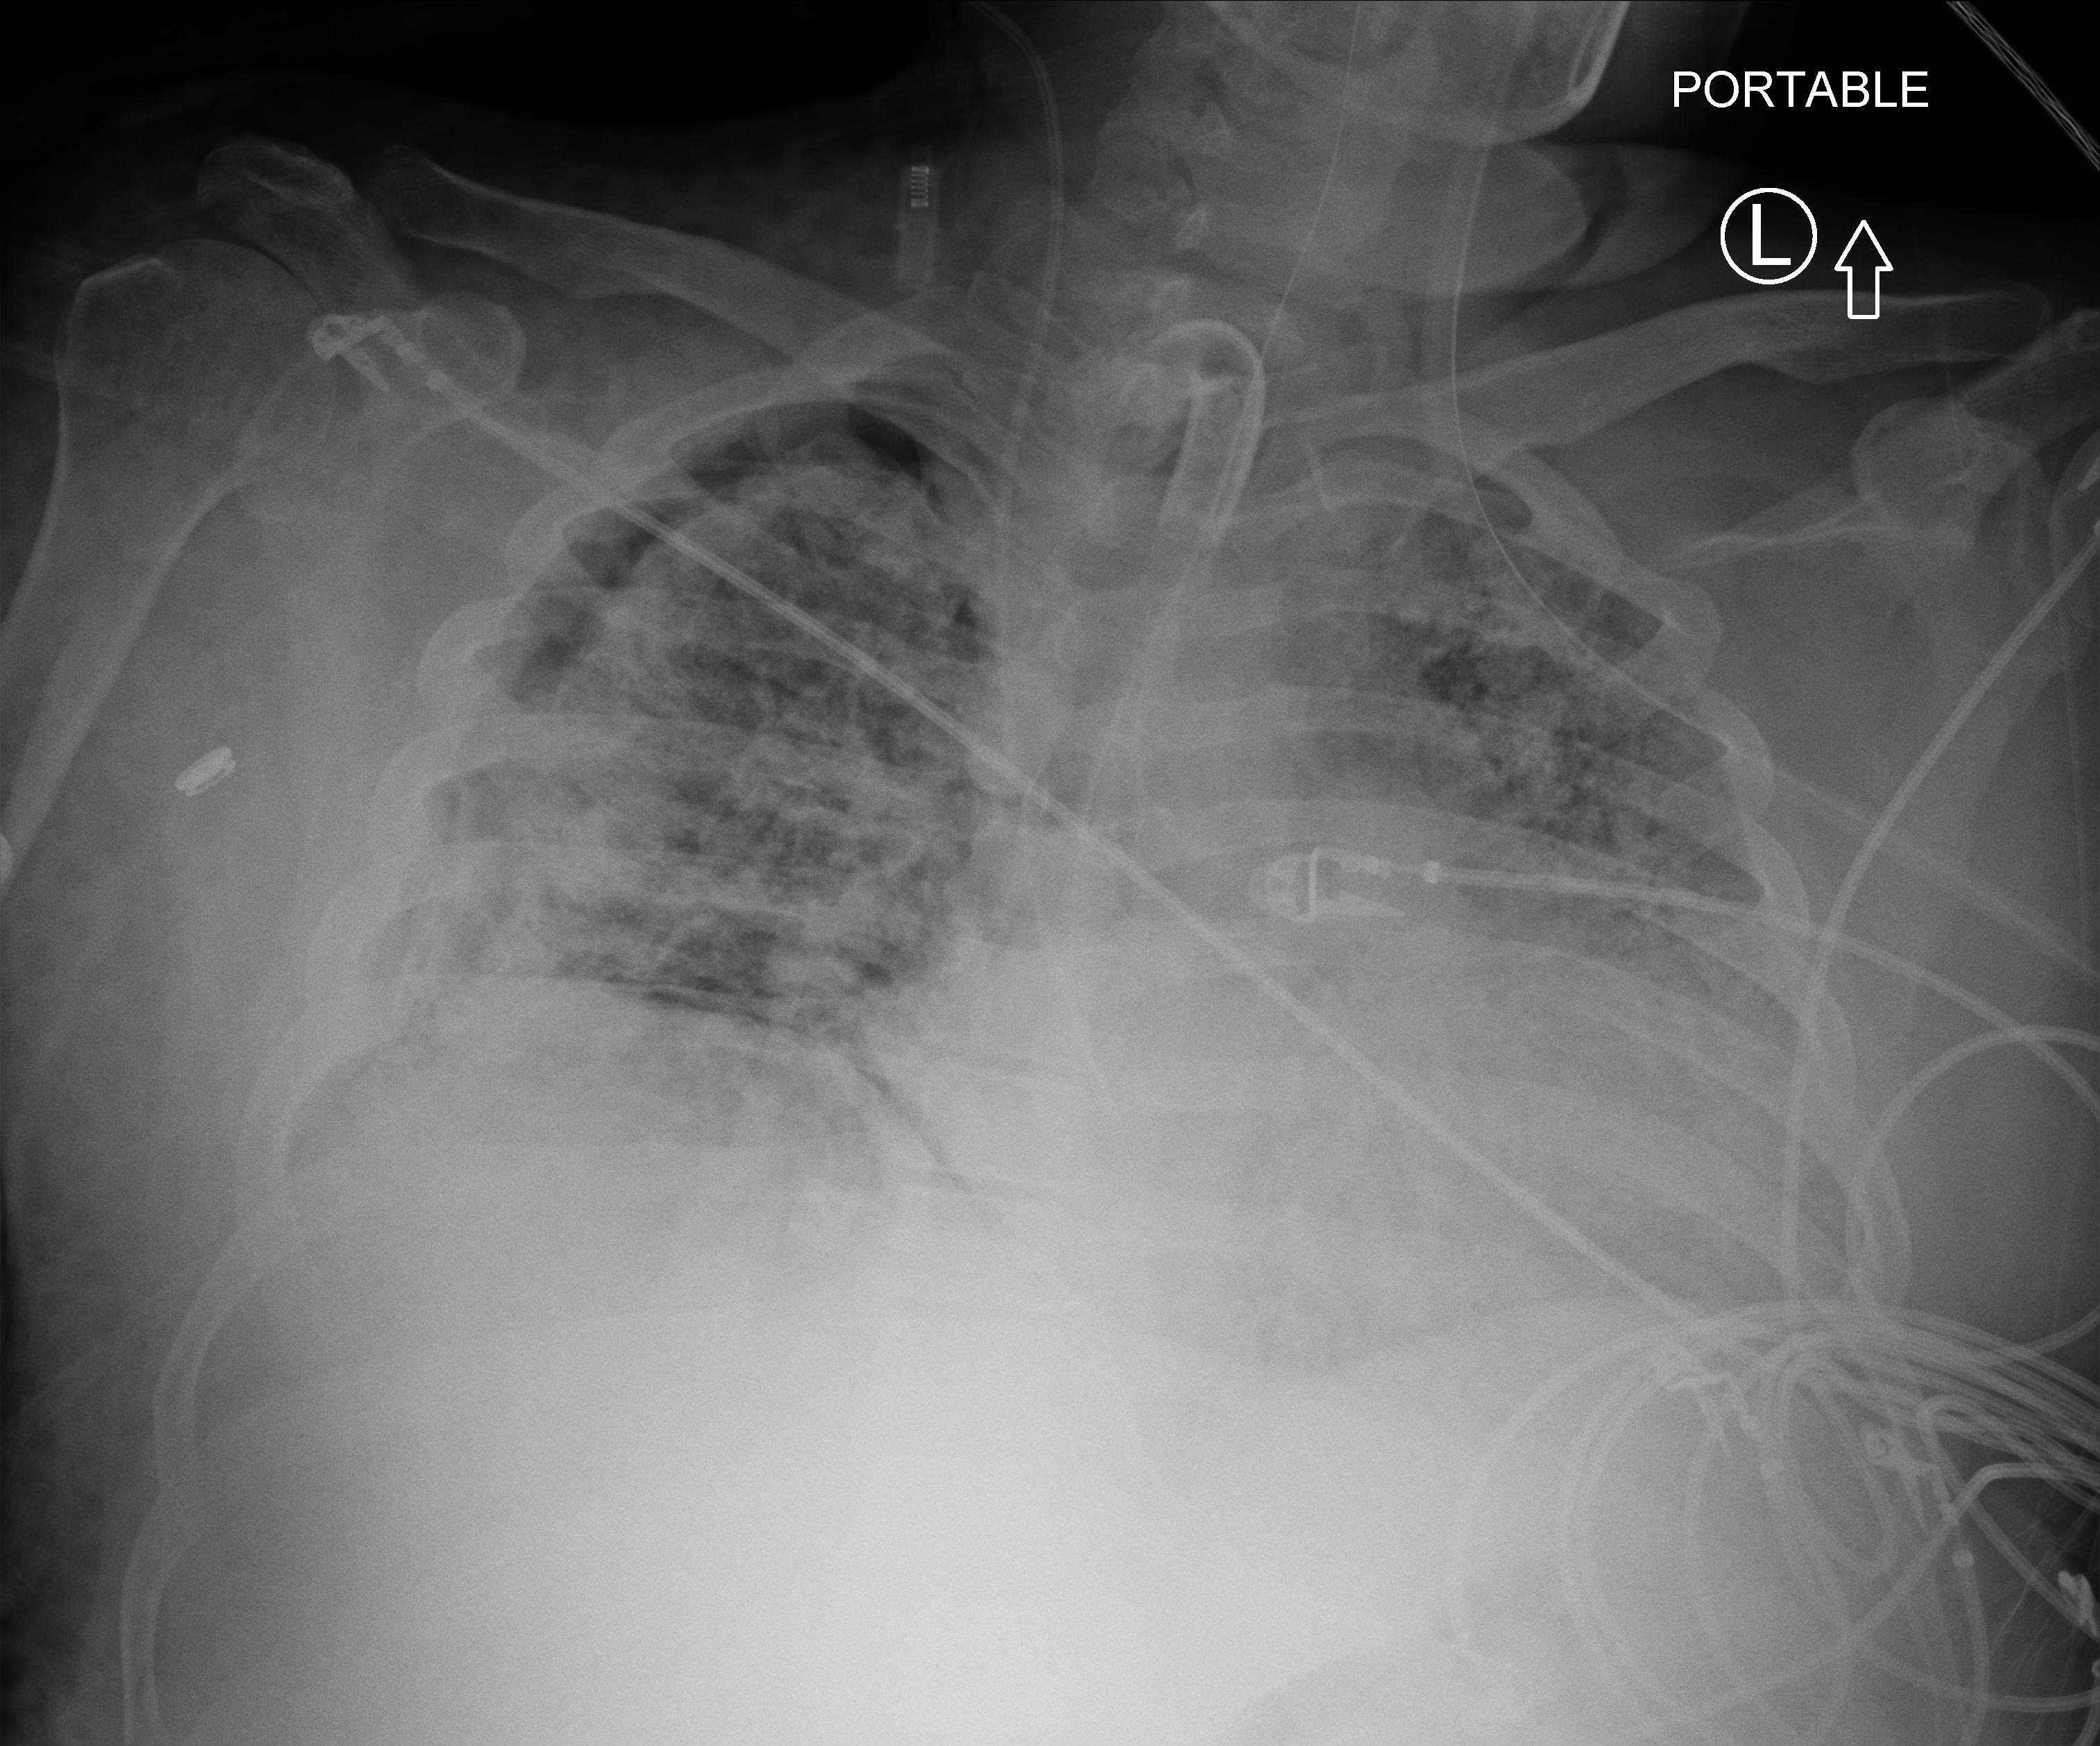
Chest X-ray (portable); anteroposterior (AP) projection. Patient hospitalised with COVID-19; male, aged 18–59 years.
Hospital-stay facts (about this admission, not read from this image; timing relative to this image not recorded): smoking status (admission record): never; mechanically ventilated during this hospital stay: yes.